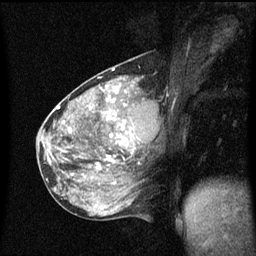
Breast MRI (dynamic contrast-enhanced), one sagittal slice; slice 24 of 60 in the series (ordered by position); dynamic contrast-enhanced series, image 2 of 3 at this slice position (ordered by acquisition); 1.5 T; TE 4.2 ms, TR 8.4 ms; 2 mm slice thickness; 256 × 256 image matrix. Patient: female, 49 years.
Structures marked on this image (semi-automatically segmented with operator editing):
- analysis volume of interest (the breast-tissue region the enhancement analysis was run in; not a lesion): box from (x=103, y=90) to (x=157, y=151) px
- tumour enhancement mask (voxels above the 70 % enhancement threshold inside the analysis volume of interest): (x=104, y=90)–(x=134, y=141)